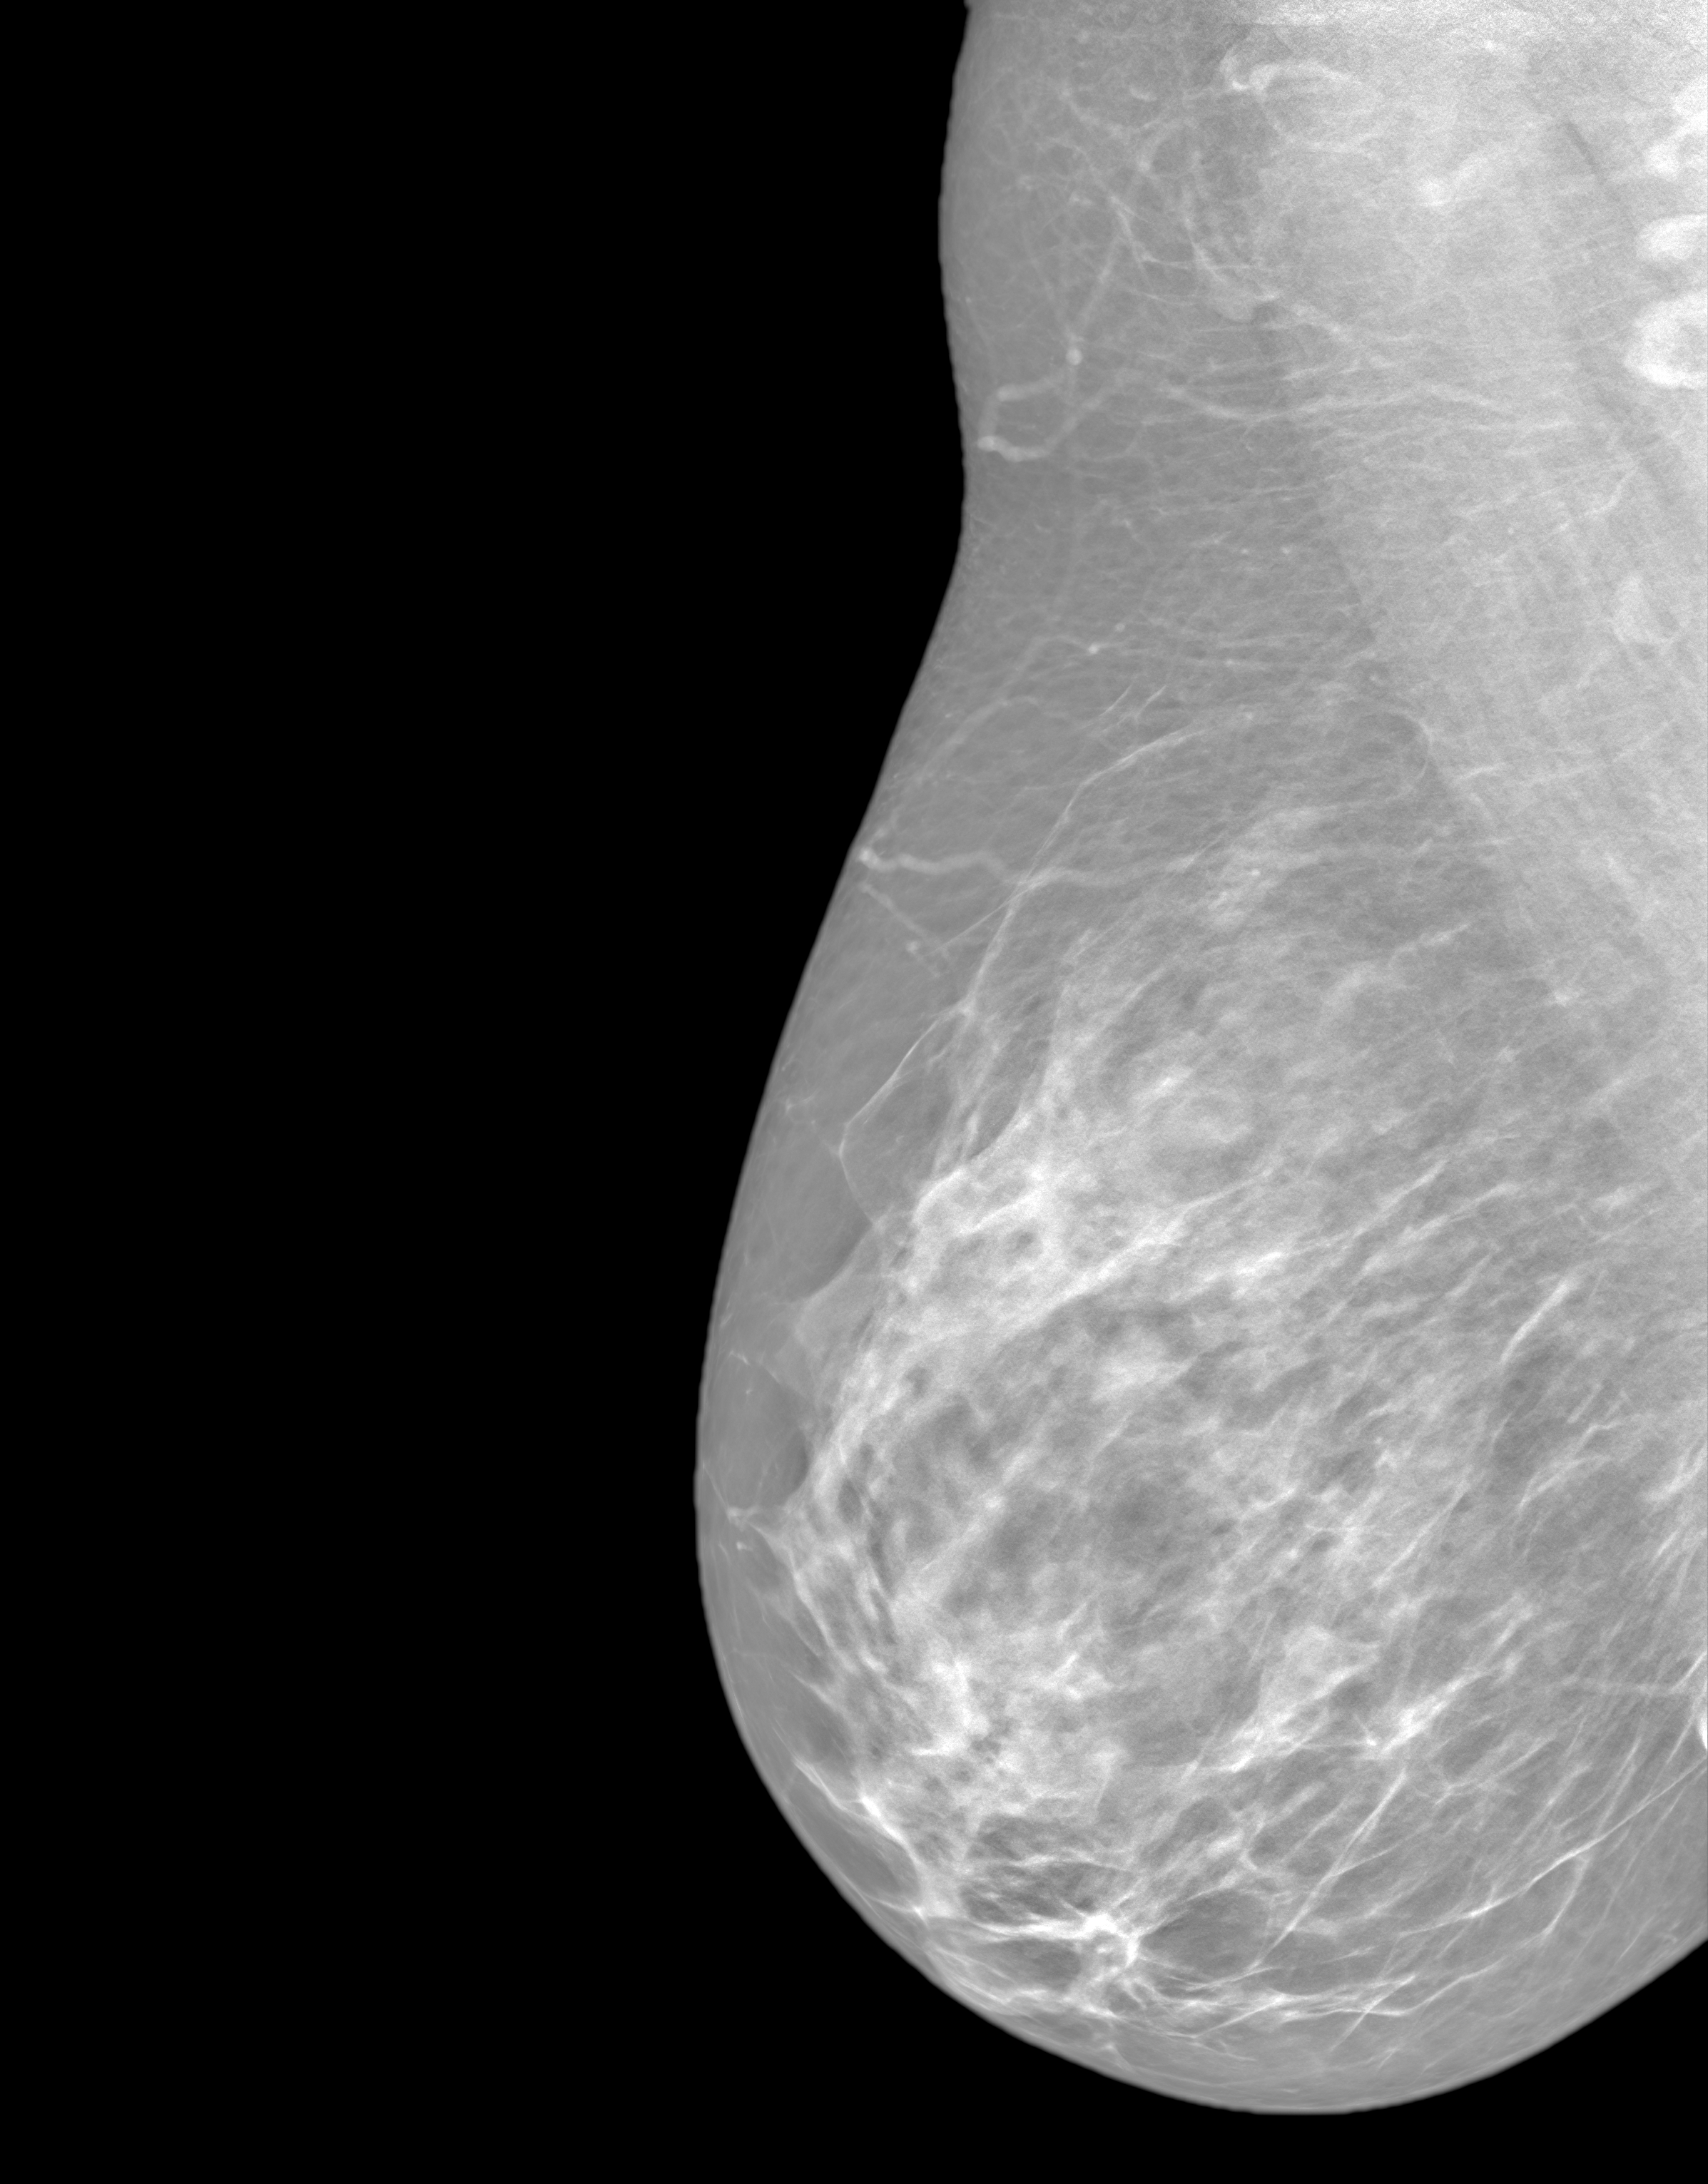
Synthesized 2-D mammogram reconstructed from digital breast tomosynthesis, right breast, mediolateral oblique (MLO) view, annual screening mammography examination. Patient: female, 42 years.
Breast density at the screening exam (both breasts): heterogeneously dense (BI-RADS density category c). Final BI-RADS assessment for this screening round (tomosynthesis exam, both breasts): category 1. Recall: no recall after this screen.